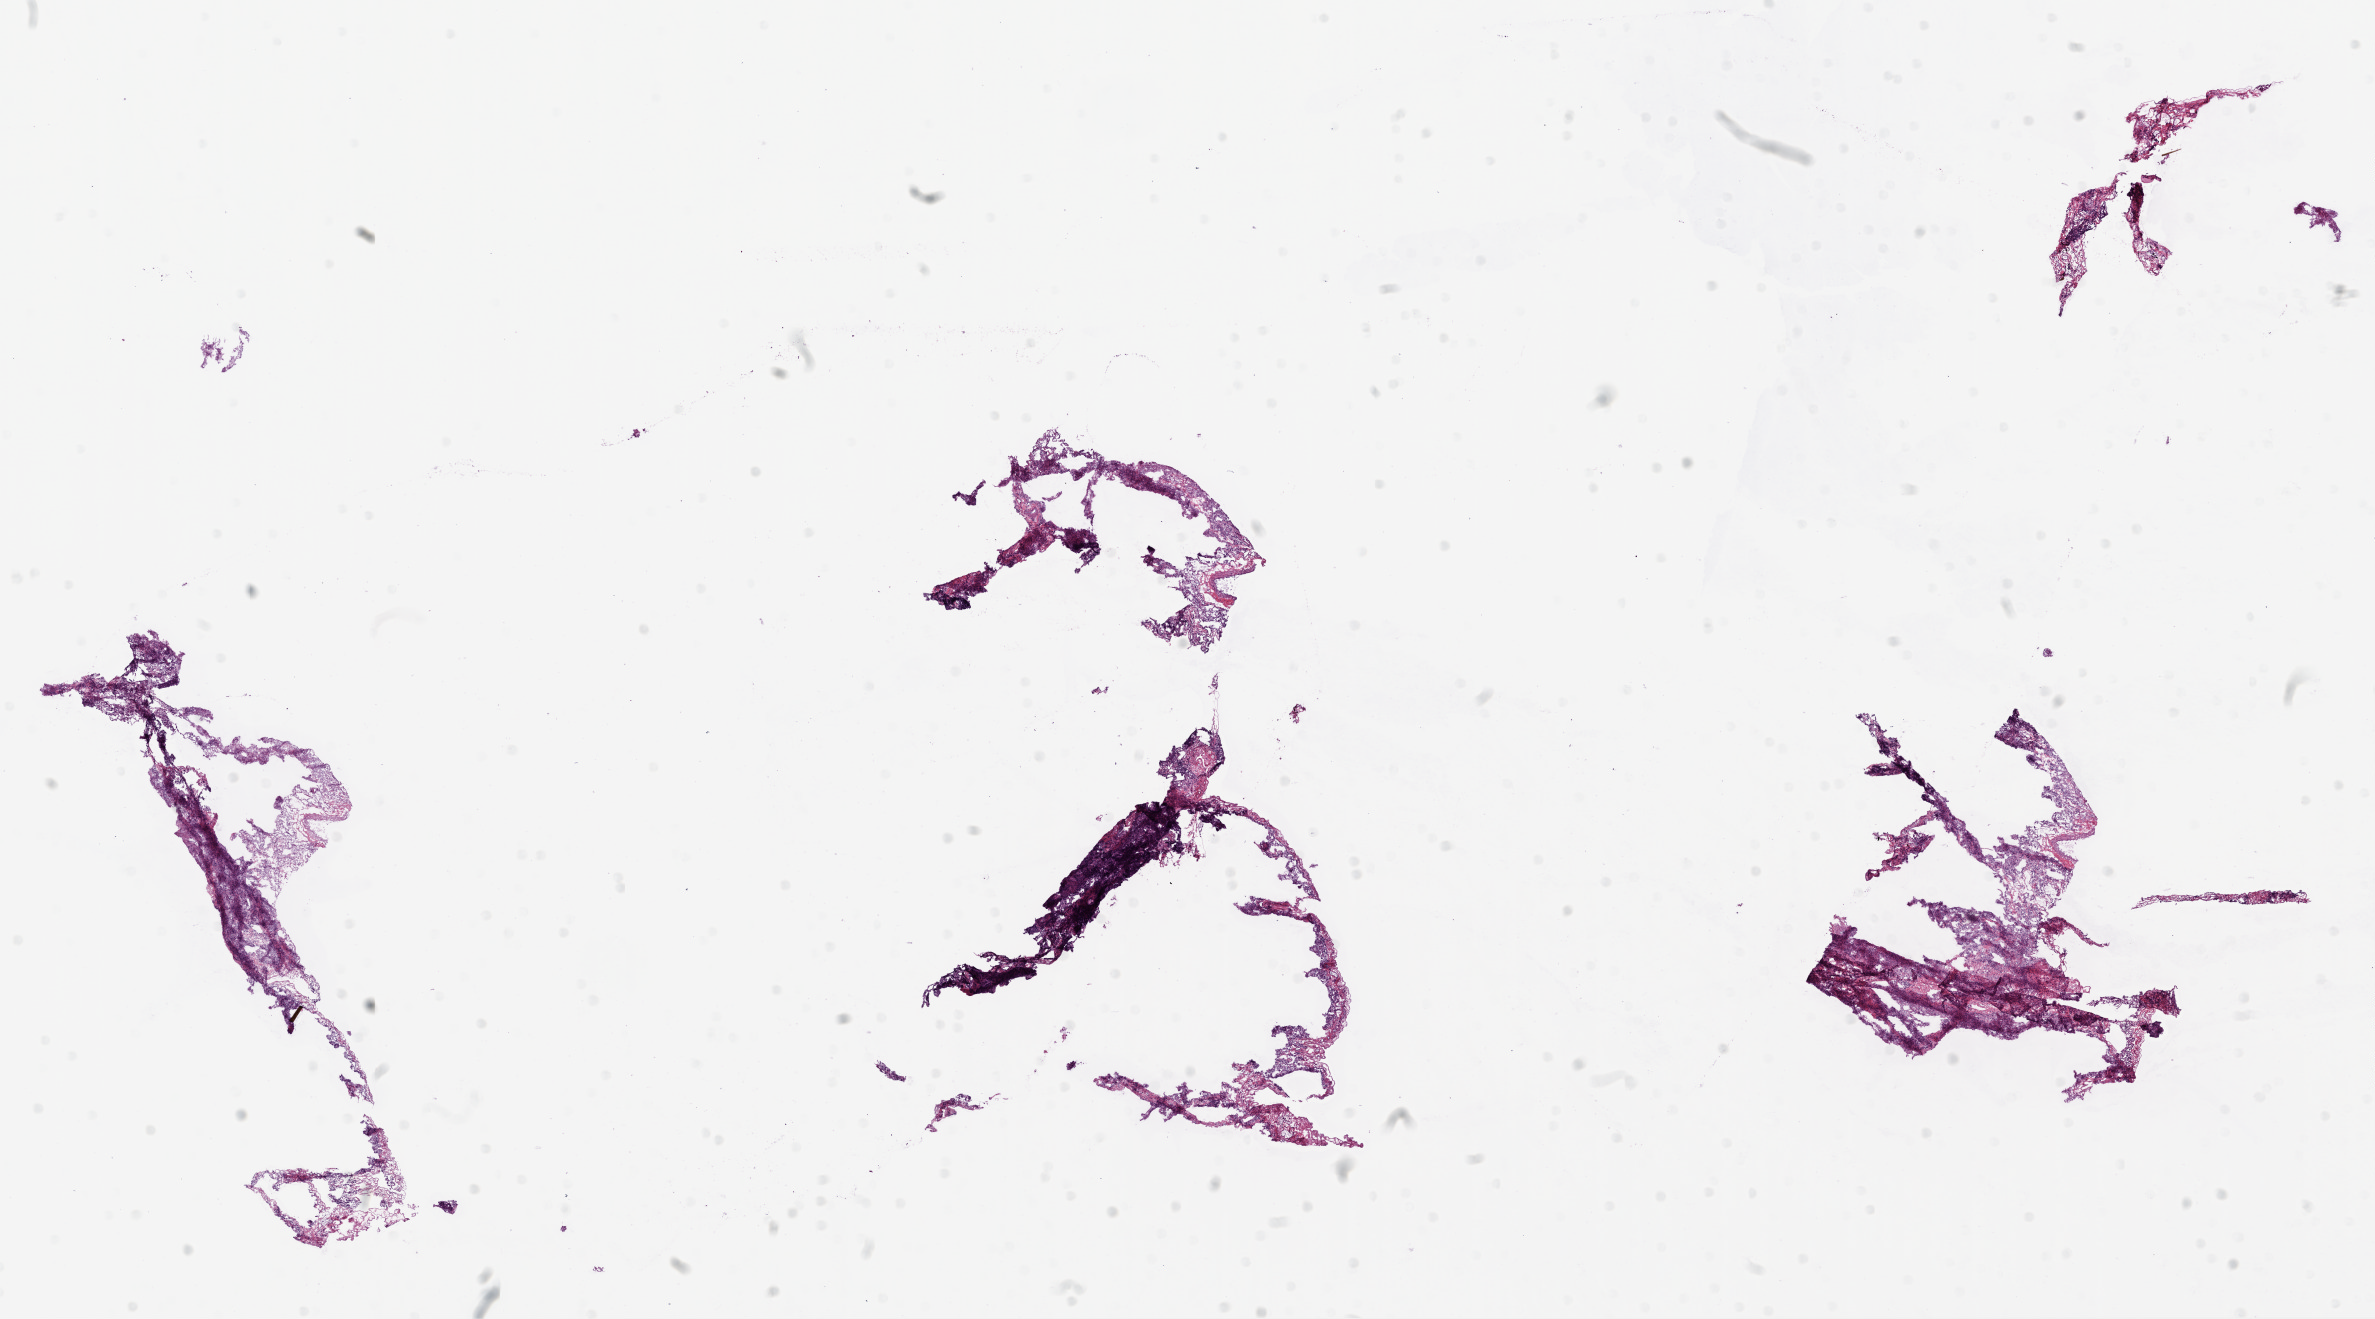
Whole-slide histology image, Hematoxylin and eosin (H&E) stained, whole scanned area (about 19.1 x 10.6 mm, acquisition: 20x scan) shown as a low-resolution overview, frozen section, solid tissue normal (non-tumour tissue) sample from the lung. Male, age 73 years at initial diagnosis.
This section: solid tissue normal sample (biorepository sample class). Patient diagnosis: Squamous cell carcinoma, NOS (lower lobe, lung).